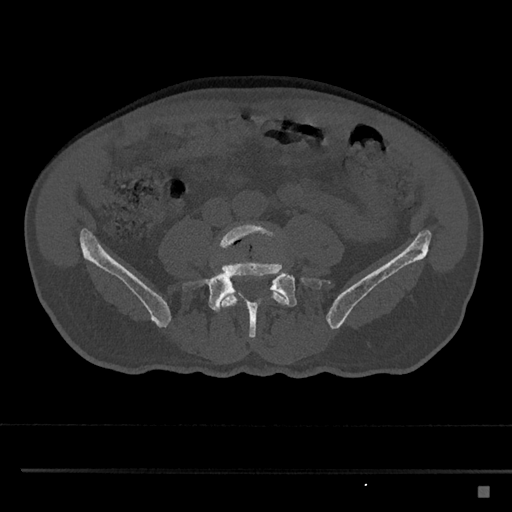
CT including the spine, one axial slice; position 602 of 797 along the scan axis; reconstruction kernel Br40s/3; 120 kVp; bone window (W 1800 / L 400 HU); 0.5 mm slice thickness; 512 × 512 image matrix, field of view 391 × 391 mm. Patient: male, 59 years. Case-level facts recorded for this patient, not image findings: primary cancer: prostate.
Annotated regions visible in this slice (semi-automatically segmented with operator editing):
- L4 vertebra: box from (x=215, y=223) to (x=289, y=312) px
- L5 vertebra: (x=180, y=253)–(x=330, y=341)